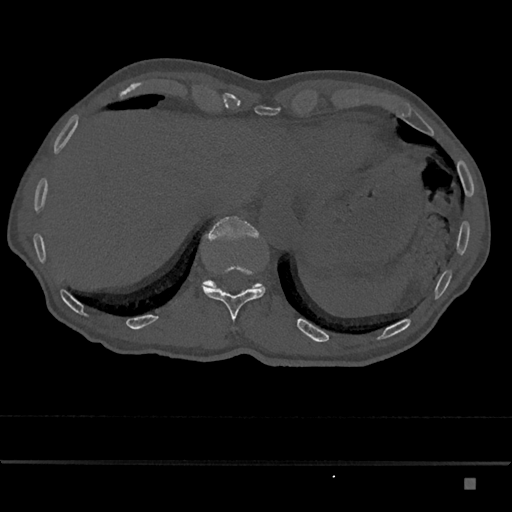
CT including the spine, one axial slice; position 662 of 797 along the scan axis; reconstruction kernel Br40s/3; 120 kVp; bone window (W 1800 / L 400 HU); 512 × 512 image matrix, field of view 390 × 390 mm. Patient: male, 72 years. From the clinical record (not read from this slice): primary cancer: prostate.
Outlined on this slice (semi-automatic segmentation, software-assisted and operator-edited):
- T11 vertebra: bounding box (x1, y1, x2, y2) in pixels: (201, 266, 266, 322)
- T12 vertebra: (203, 216, 263, 288)